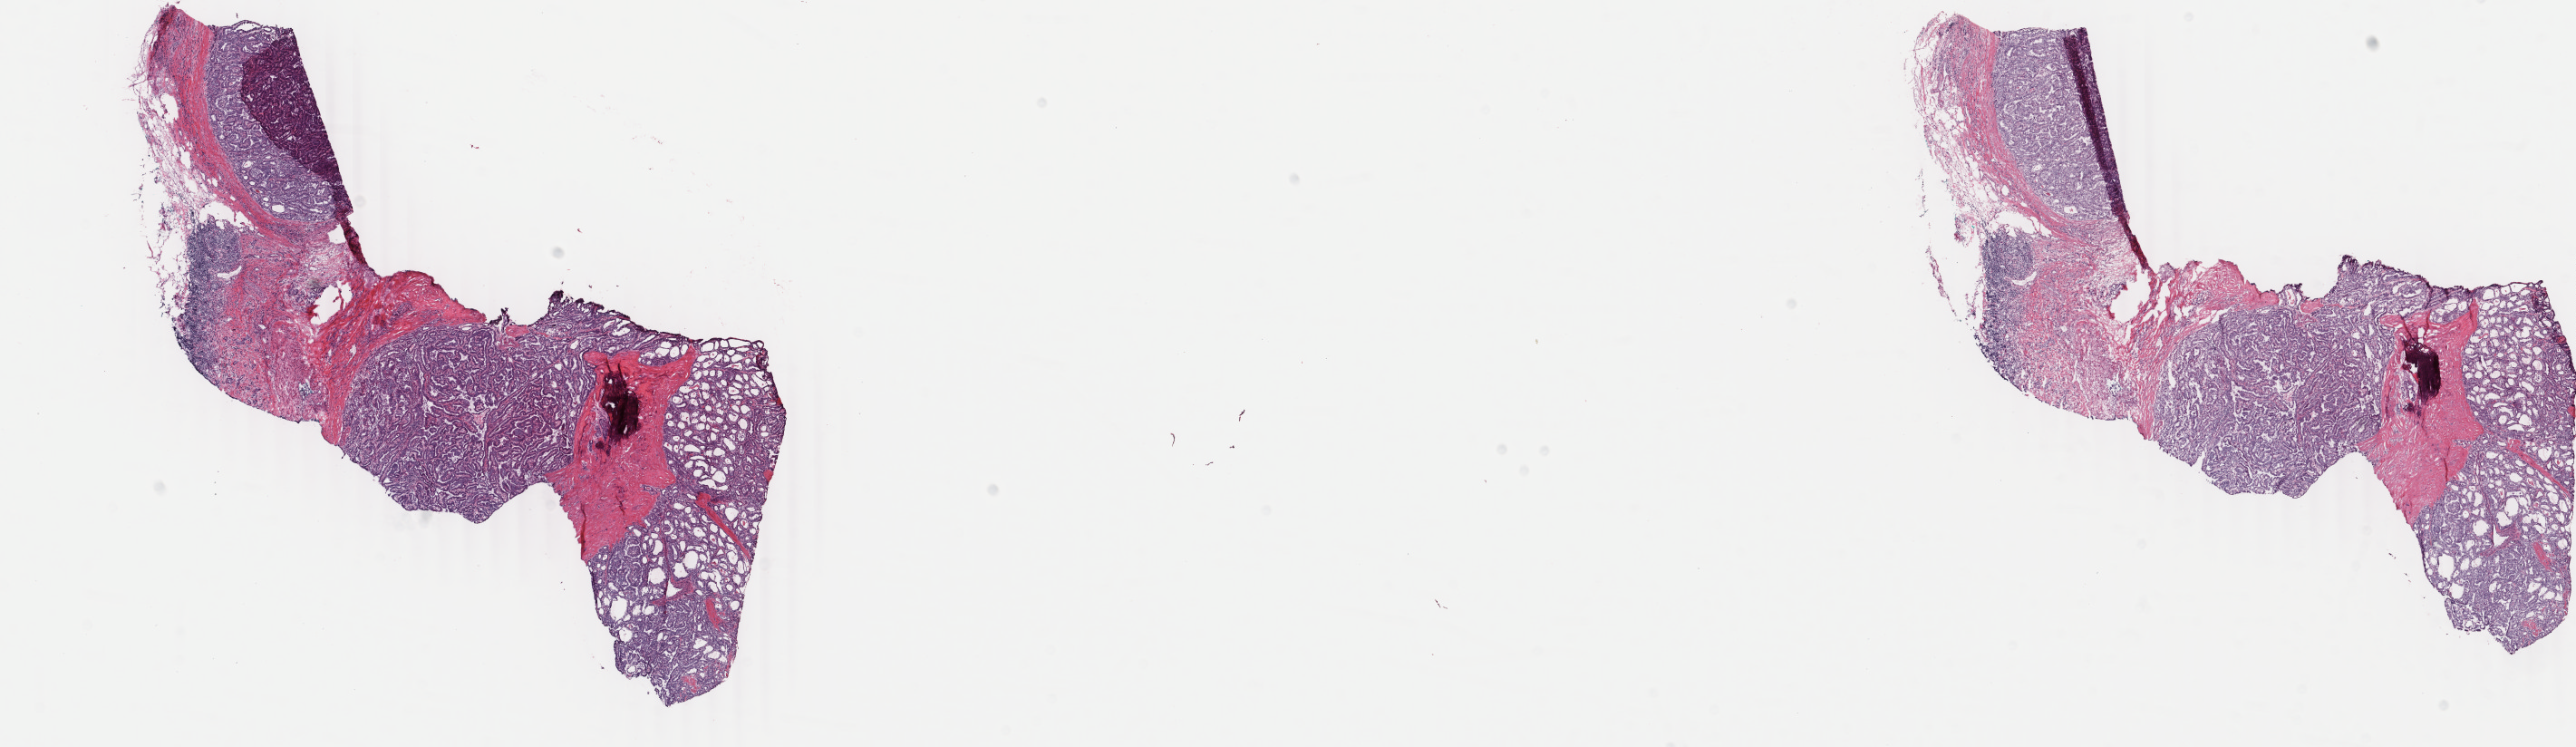
Hematoxylin and eosin (H&E) stained whole-slide image, shown as a low-resolution overview of the whole scanned area (about 22.6 x 6.6 mm); frozen section; thyroid, primary tumour sample. Female, age 65 years at initial diagnosis. Slide review estimates, as recorded: tumour cells 70%, tumour nuclei 85%, normal cells 0%, stromal cells 30%, necrosis 0%. Infiltration values recorded for this section: lymphocyte infiltration 10%, monocyte infiltration 0%, neutrophil infiltration 0%.
* AJCC pathologic stage: III (6th edition)
* lymph nodes positive (case pathology): 5 of 7 examined
* pathologic diagnosis: Papillary adenocarcinoma, NOS (thyroid gland)